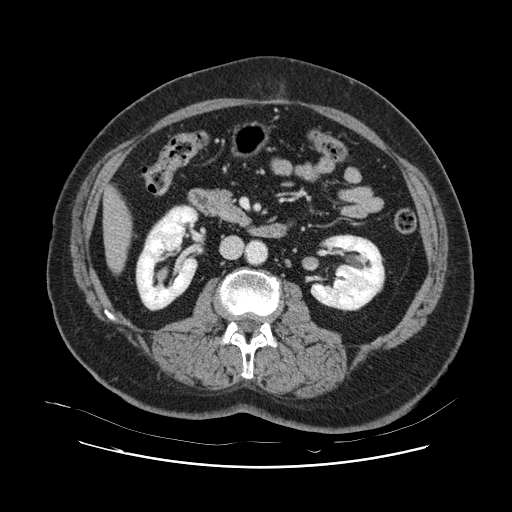
Contrast-enhanced abdominal CT, one axial slice; slice 25 of 132 in the series (ordered by position); 120 kVp; intravenous contrast given; soft-tissue window (W 400 / L 40 HU); 2.5 mm slice thickness; 512 × 512 image matrix, field of view 391 × 391 mm. Female patient, age 73 years. From the clinical record (not read from this slice): diagnosis: colorectal cancer liver metastases, imaged before liver resection; multiple liver metastases: no; largest metastasis: 7 cm.
Outlined on this slice (outlined manually by an expert reader):
- liver: bounding box (x1, y1, x2, y2) in pixels: (104, 190, 130, 271)
- planned liver remnant (the part of the liver to remain after resection): (105, 191, 131, 272)